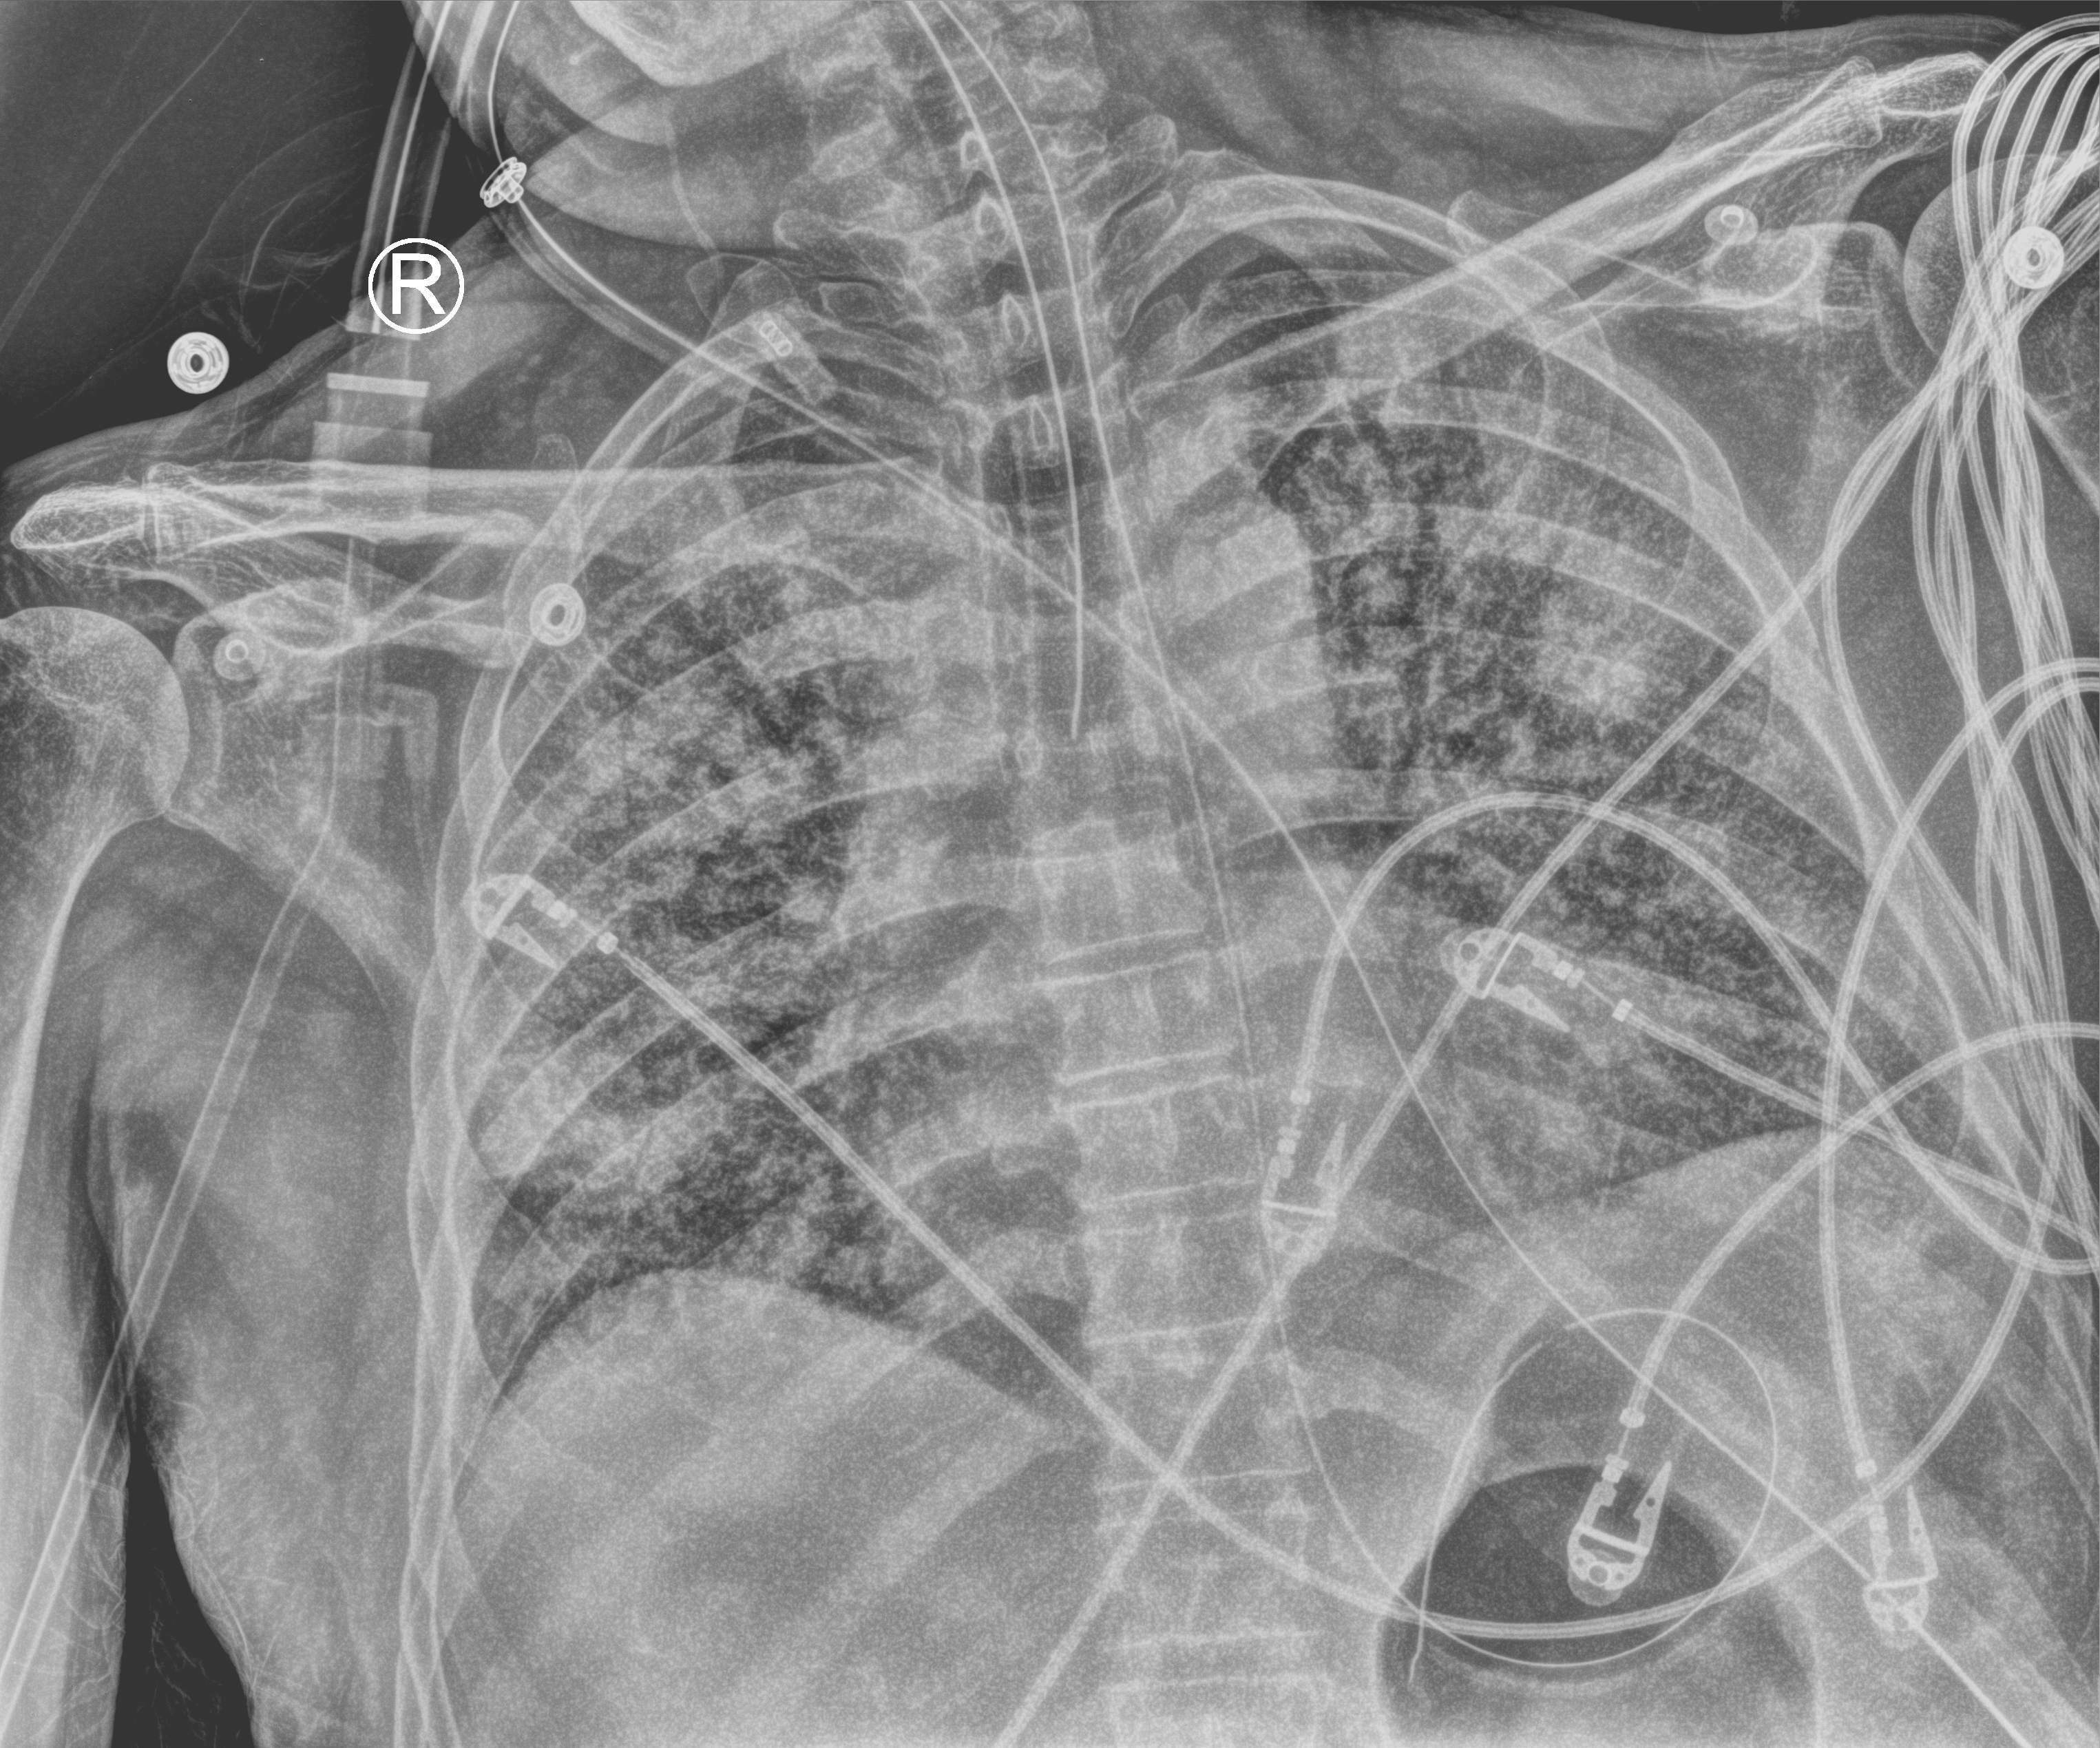
Bedside chest radiograph (computed radiography); anteroposterior (AP) projection. Patient hospitalised with COVID-19; male, aged 60–74 years.
From the hospital-stay record, not from the radiograph (when in the stay this image was taken is not recorded):
- mechanically ventilated during this hospital stay: yes
- admitted to intensive care during this hospital stay: yes